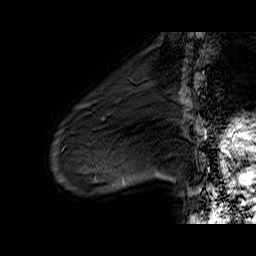
Breast MRI (dynamic contrast-enhanced), one sagittal slice; slice 12 of 60 in the series (ordered by position); dynamic contrast-enhanced series, time point 2 of 6 at this slice position (early post-contrast); 1.5 T; TE 6.5 ms, TR 32.9 ms; 4 mm slice thickness; 256 × 256 image matrix. Female patient. Case-level facts recorded for this patient, not image findings: setting: breast cancer imaged before/during neoadjuvant chemotherapy; receptor status: HER2-positive.
Outlined on this slice (semi-automatic segmentation, software-assisted and operator-edited):
- analysis volume of interest (the breast-tissue region the enhancement analysis was run in; not a lesion): box from (x=72, y=88) to (x=133, y=137) px
- tumour enhancement mask (voxels above the 100 % enhancement threshold inside the analysis volume of interest): (x=76, y=103)–(x=104, y=119)